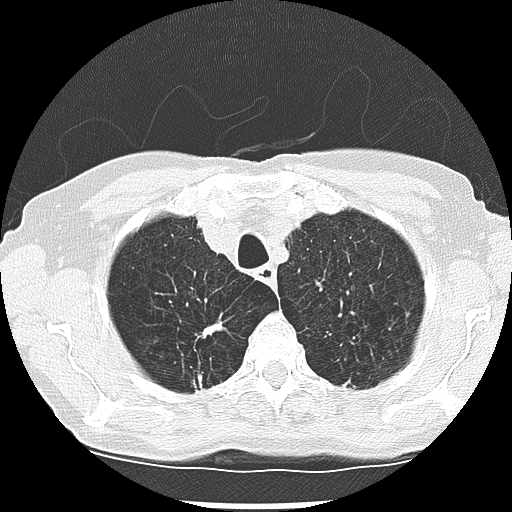
Low-dose screening chest CT, one axial slice; position 228 of 265 along the scan axis; 120 kVp; lung window (W 1500 / L -600 HU); 2.5 mm slice thickness; 512 × 512 image matrix, field of view 300 × 300 mm.
Structures marked on this image (outlined manually by an expert reader):
- lesion 1 (nodule, upper lobe of right lung): bounding box (x1, y1, x2, y2) in pixels: (198, 377, 202, 381)
- lesion 2 (tumor, upper lobe of right lung): (203, 324, 222, 336)